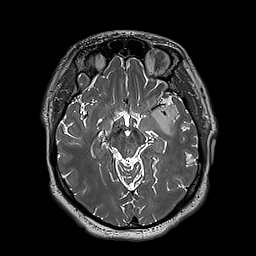
Brain MRI from a brain-tumour surgery series, one axial slice; 1 mm slice thickness; 256 × 256 image matrix, field of view 250 × 250 mm. Case-level facts recorded for this patient, not image findings: histopathology: Astrocytoma; WHO grade: 3; IDH mutation: yes; tumour location: Left Insular.
Structures marked on this image (outlined manually by an expert reader):
- tumour: bounding box [x1, y1, x2, y2] px = [152, 99, 179, 136]